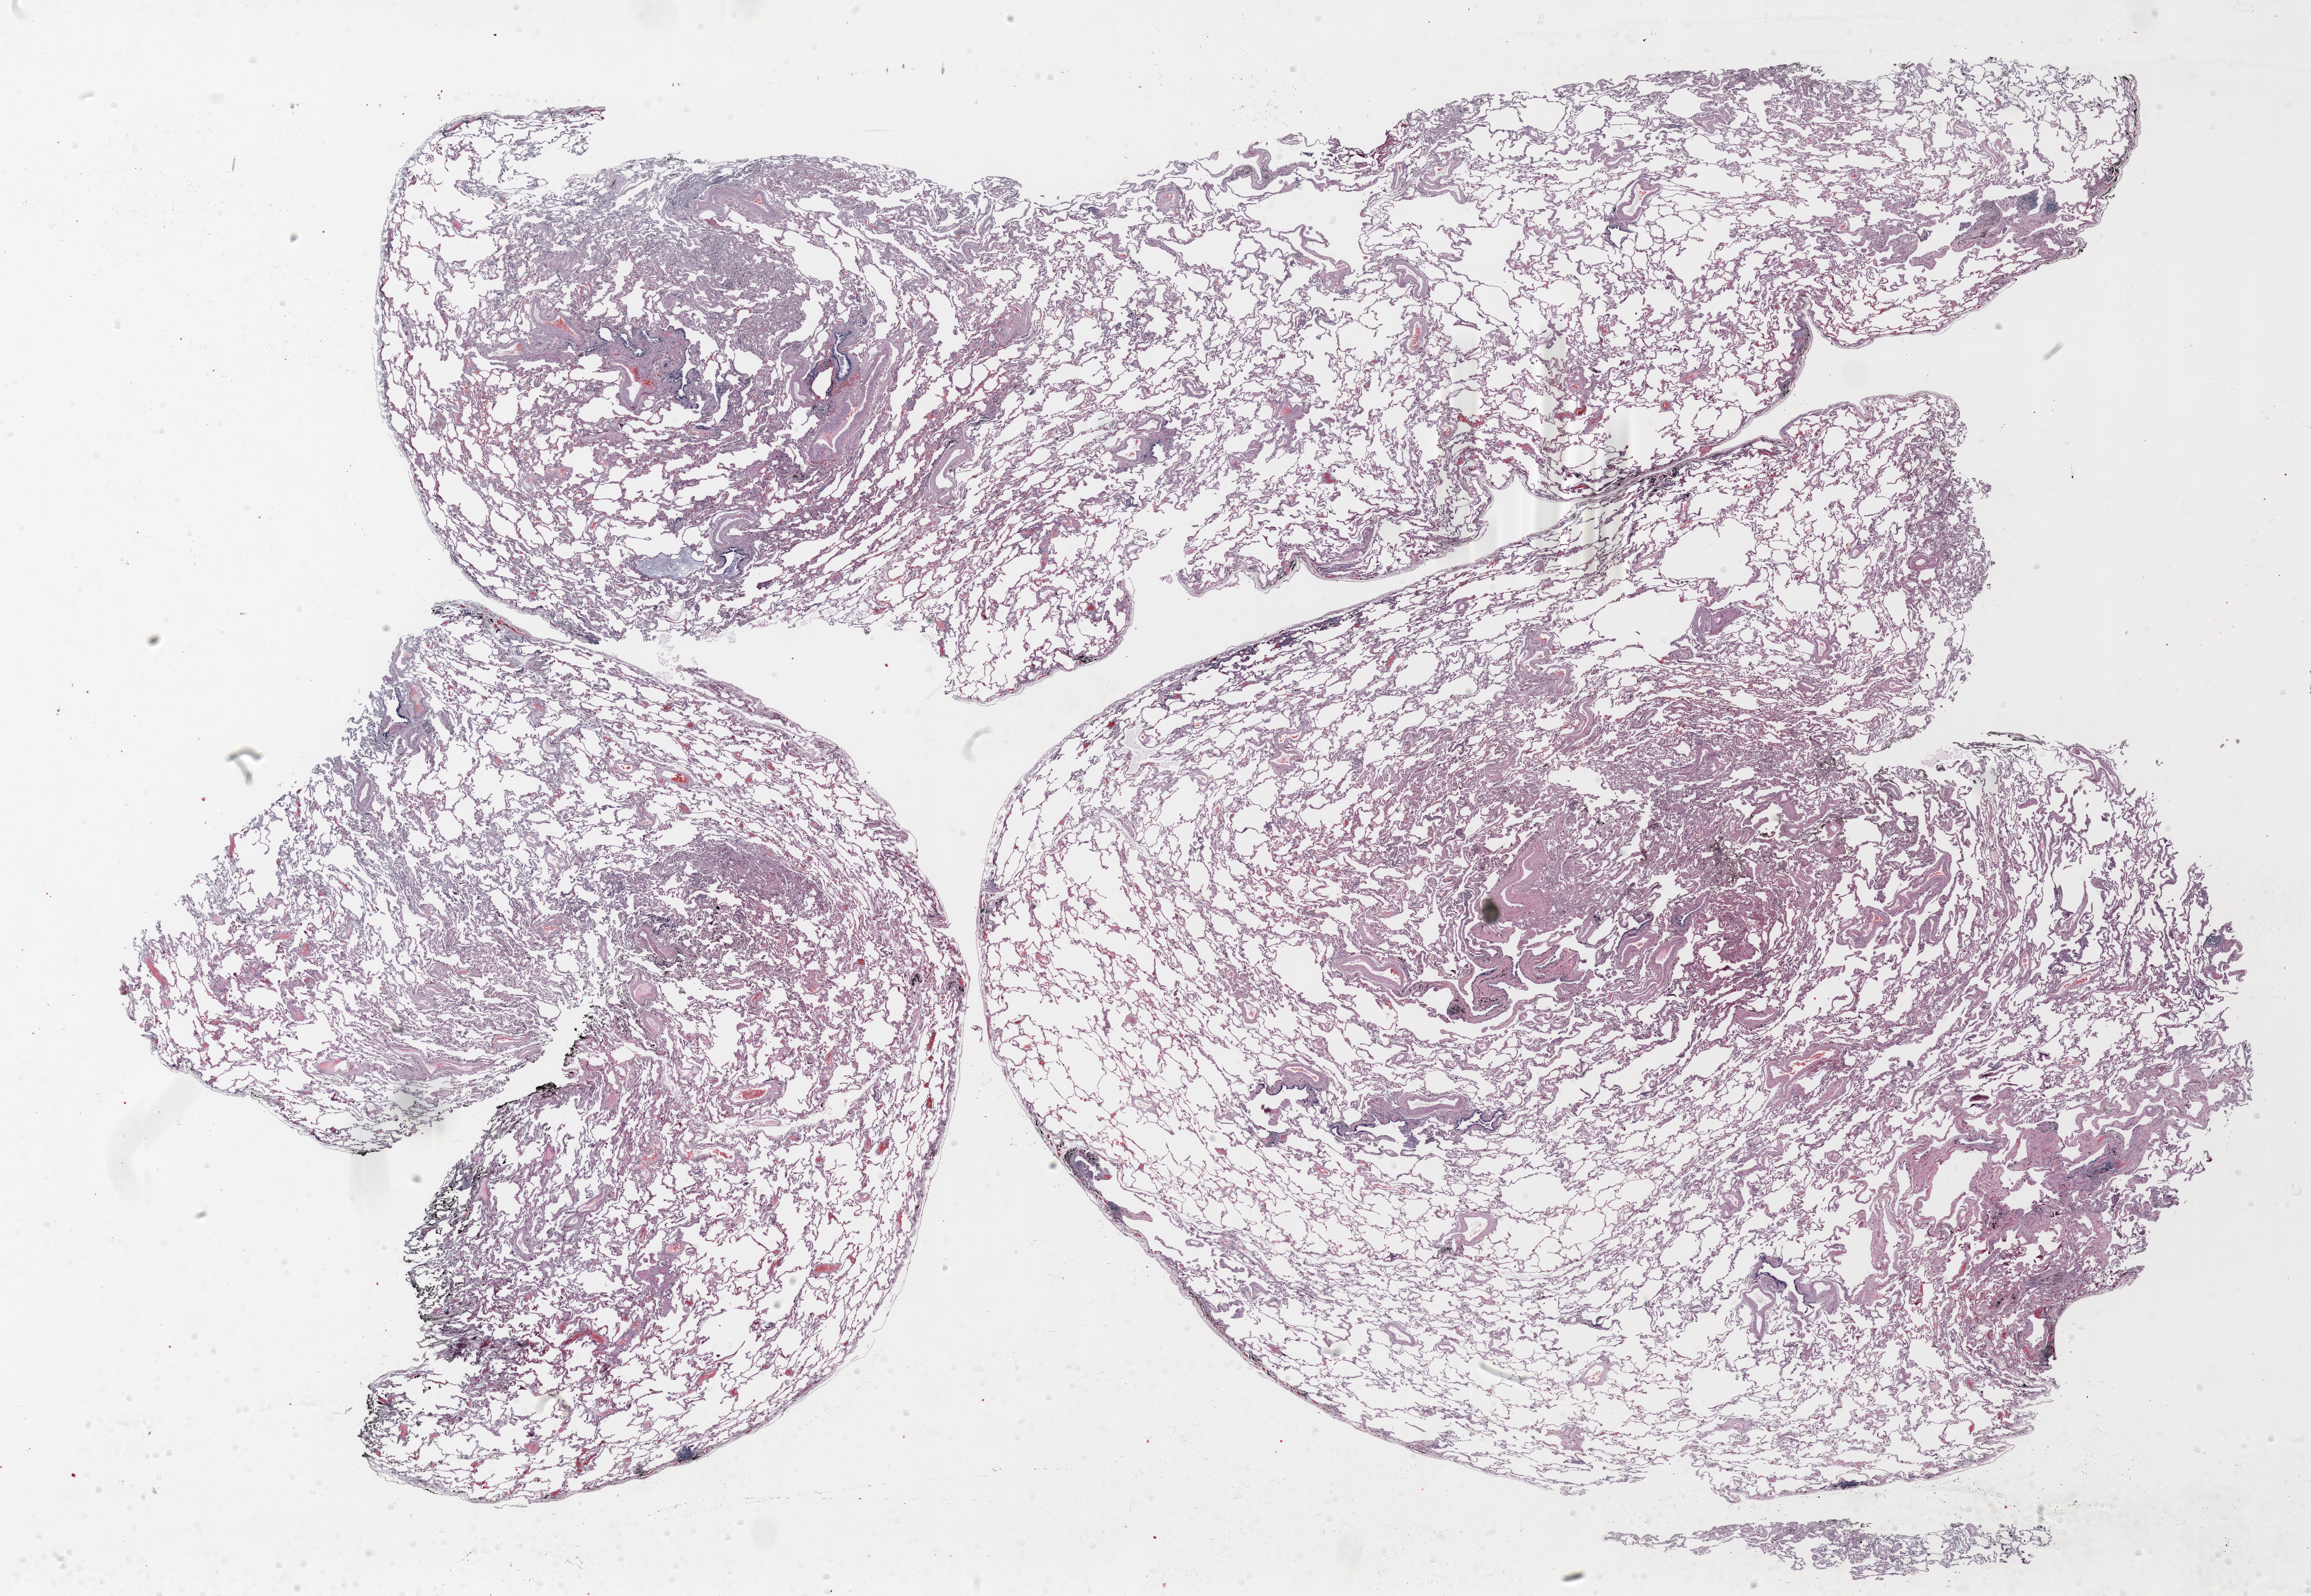
H&E whole-slide image — whole scanned area (about 32.0 x 22.1 mm) shown as a low-resolution overview, formalin-fixed paraffin-embedded (FFPE) section, lung. Female patient, aged 74 at enrolment. Grade: poorly differentiated (G3).
* participant's lung-cancer diagnosis: Bronchiolo-alveolar adenocarcinoma, NOS (ICD-O-3 8250/3)
* stage (AJCC 6th edition): IV
* primary tumour location (clinical record): other location
* tumour size (pathology): 18 mm